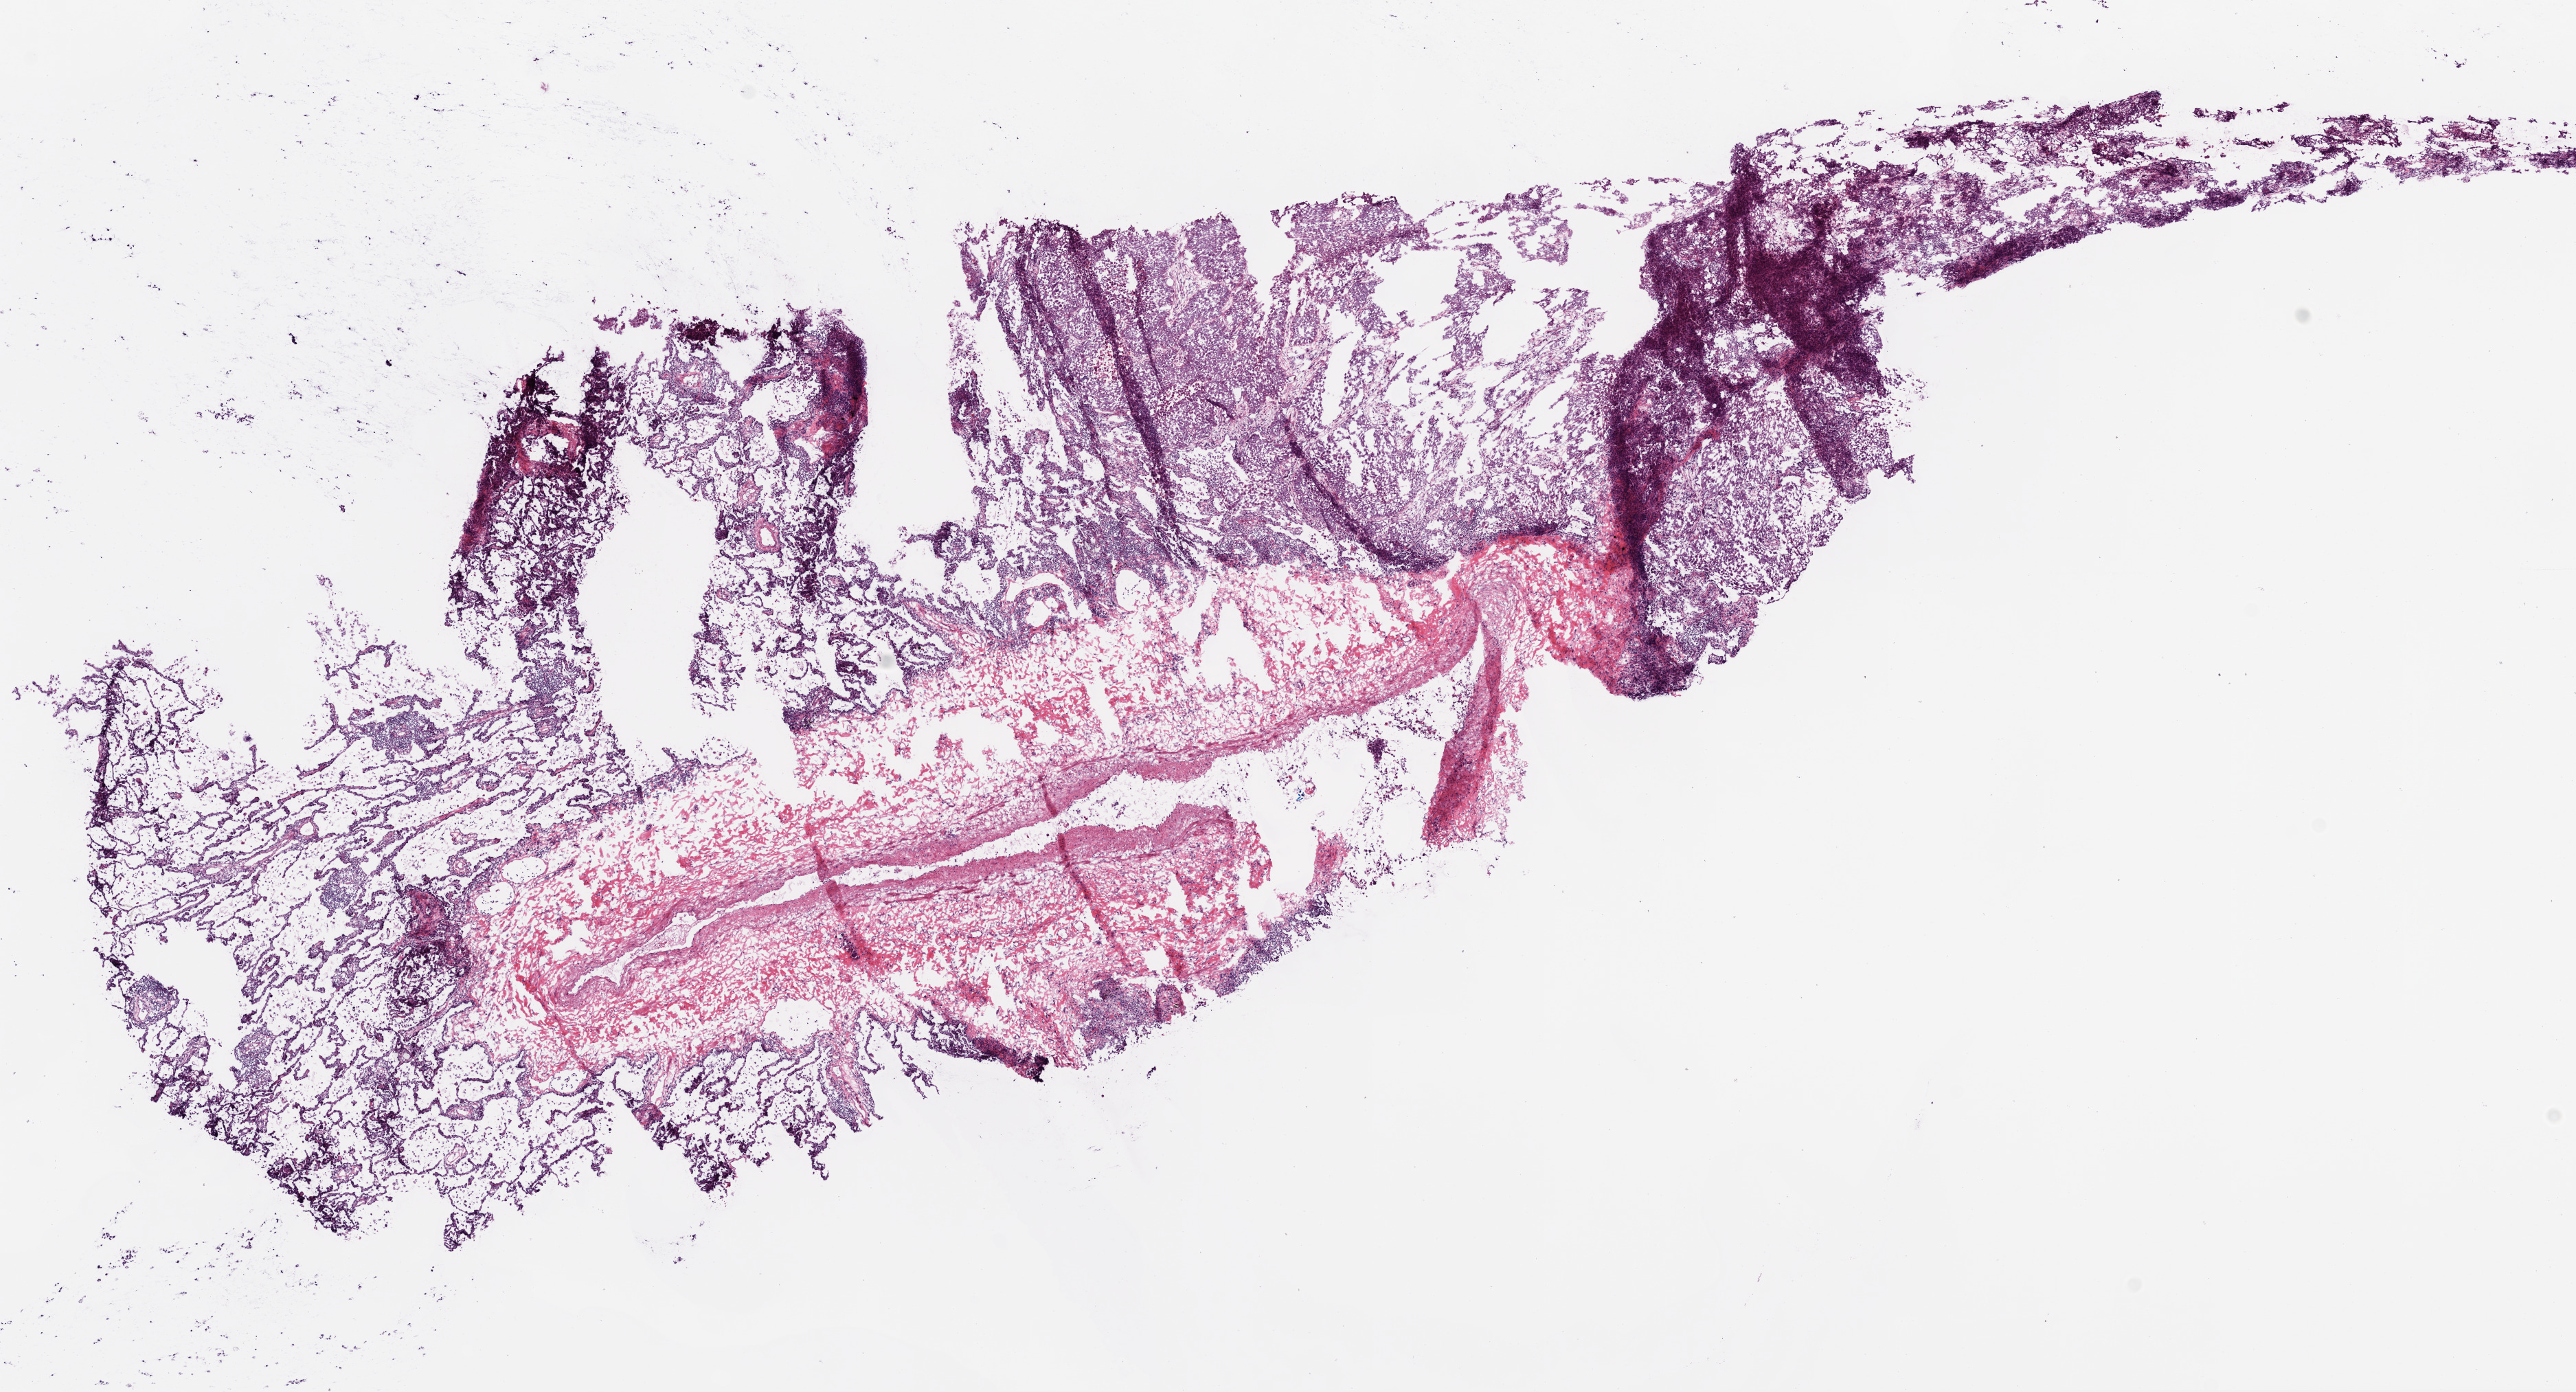
Digitized Hematoxylin and eosin (H&E) stained tissue section (whole slide) — whole scanned area (about 15.0 x 8.1 mm) shown as a low-resolution overview; frozen section from the bottom of the tissue portion; lung, primary tumour sample. Male, age 81 years at initial diagnosis. Composition of this section per pathologist review: tumour cells 75%, tumour nuclei 80%.
Pathologic diagnosis: Squamous cell carcinoma, NOS (lower lobe, lung).